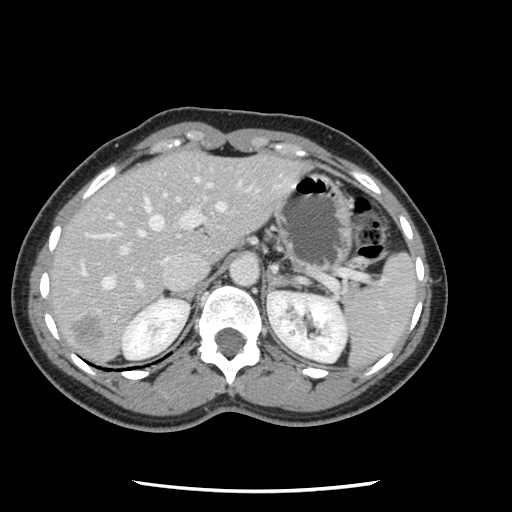
Contrast-enhanced abdominal CT, one axial slice. Slice 84 of 134 in the series (ordered by position). 120 kVp. Soft-tissue window (W 400 / L 40 HU). 512 × 512 image matrix. Female patient, age 43 years. Case-level facts recorded for this patient, not image findings: diagnosis: colorectal cancer liver metastases, imaged before liver resection; multiple liver metastases: yes; largest metastasis: 3.4 cm; disease in both lobes: yes.
Outlined on this slice (manually delineated by an expert):
- hepatic veins: bounding box [x1, y1, x2, y2] px = [81, 177, 227, 290]
- liver: [49, 153, 305, 364]
- planned liver remnant (the part of the liver to remain after resection): [49, 156, 190, 308]
- portal vein (with intrahepatic branches): [103, 183, 281, 294]
- liver metastasis: [73, 316, 105, 347]